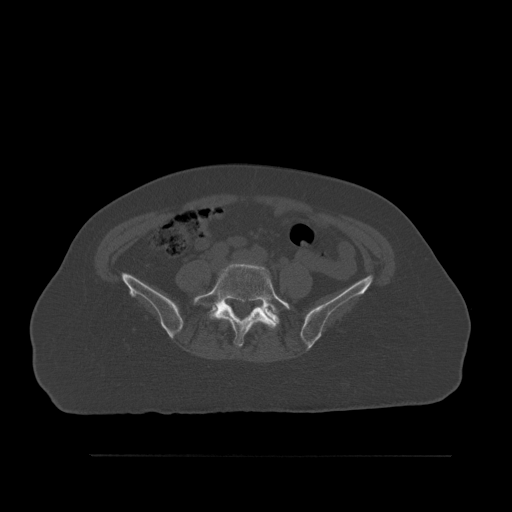
CT including the spine, one axial slice. Position 189 of 527 along the scan axis. Bone window (W 1800 / L 400 HU). 512 × 512 image matrix, field of view 470 × 470 mm. Patient: female, 73 years. From the clinical record (not read from this slice): primary cancer: breast; vertebrae with lytic lesions (as recorded): L2.
Annotated regions visible in this slice (semi-automatically segmented with operator editing):
- L5 vertebra: bounding box (x1, y1, x2, y2) in pixels: (193, 263, 291, 347)